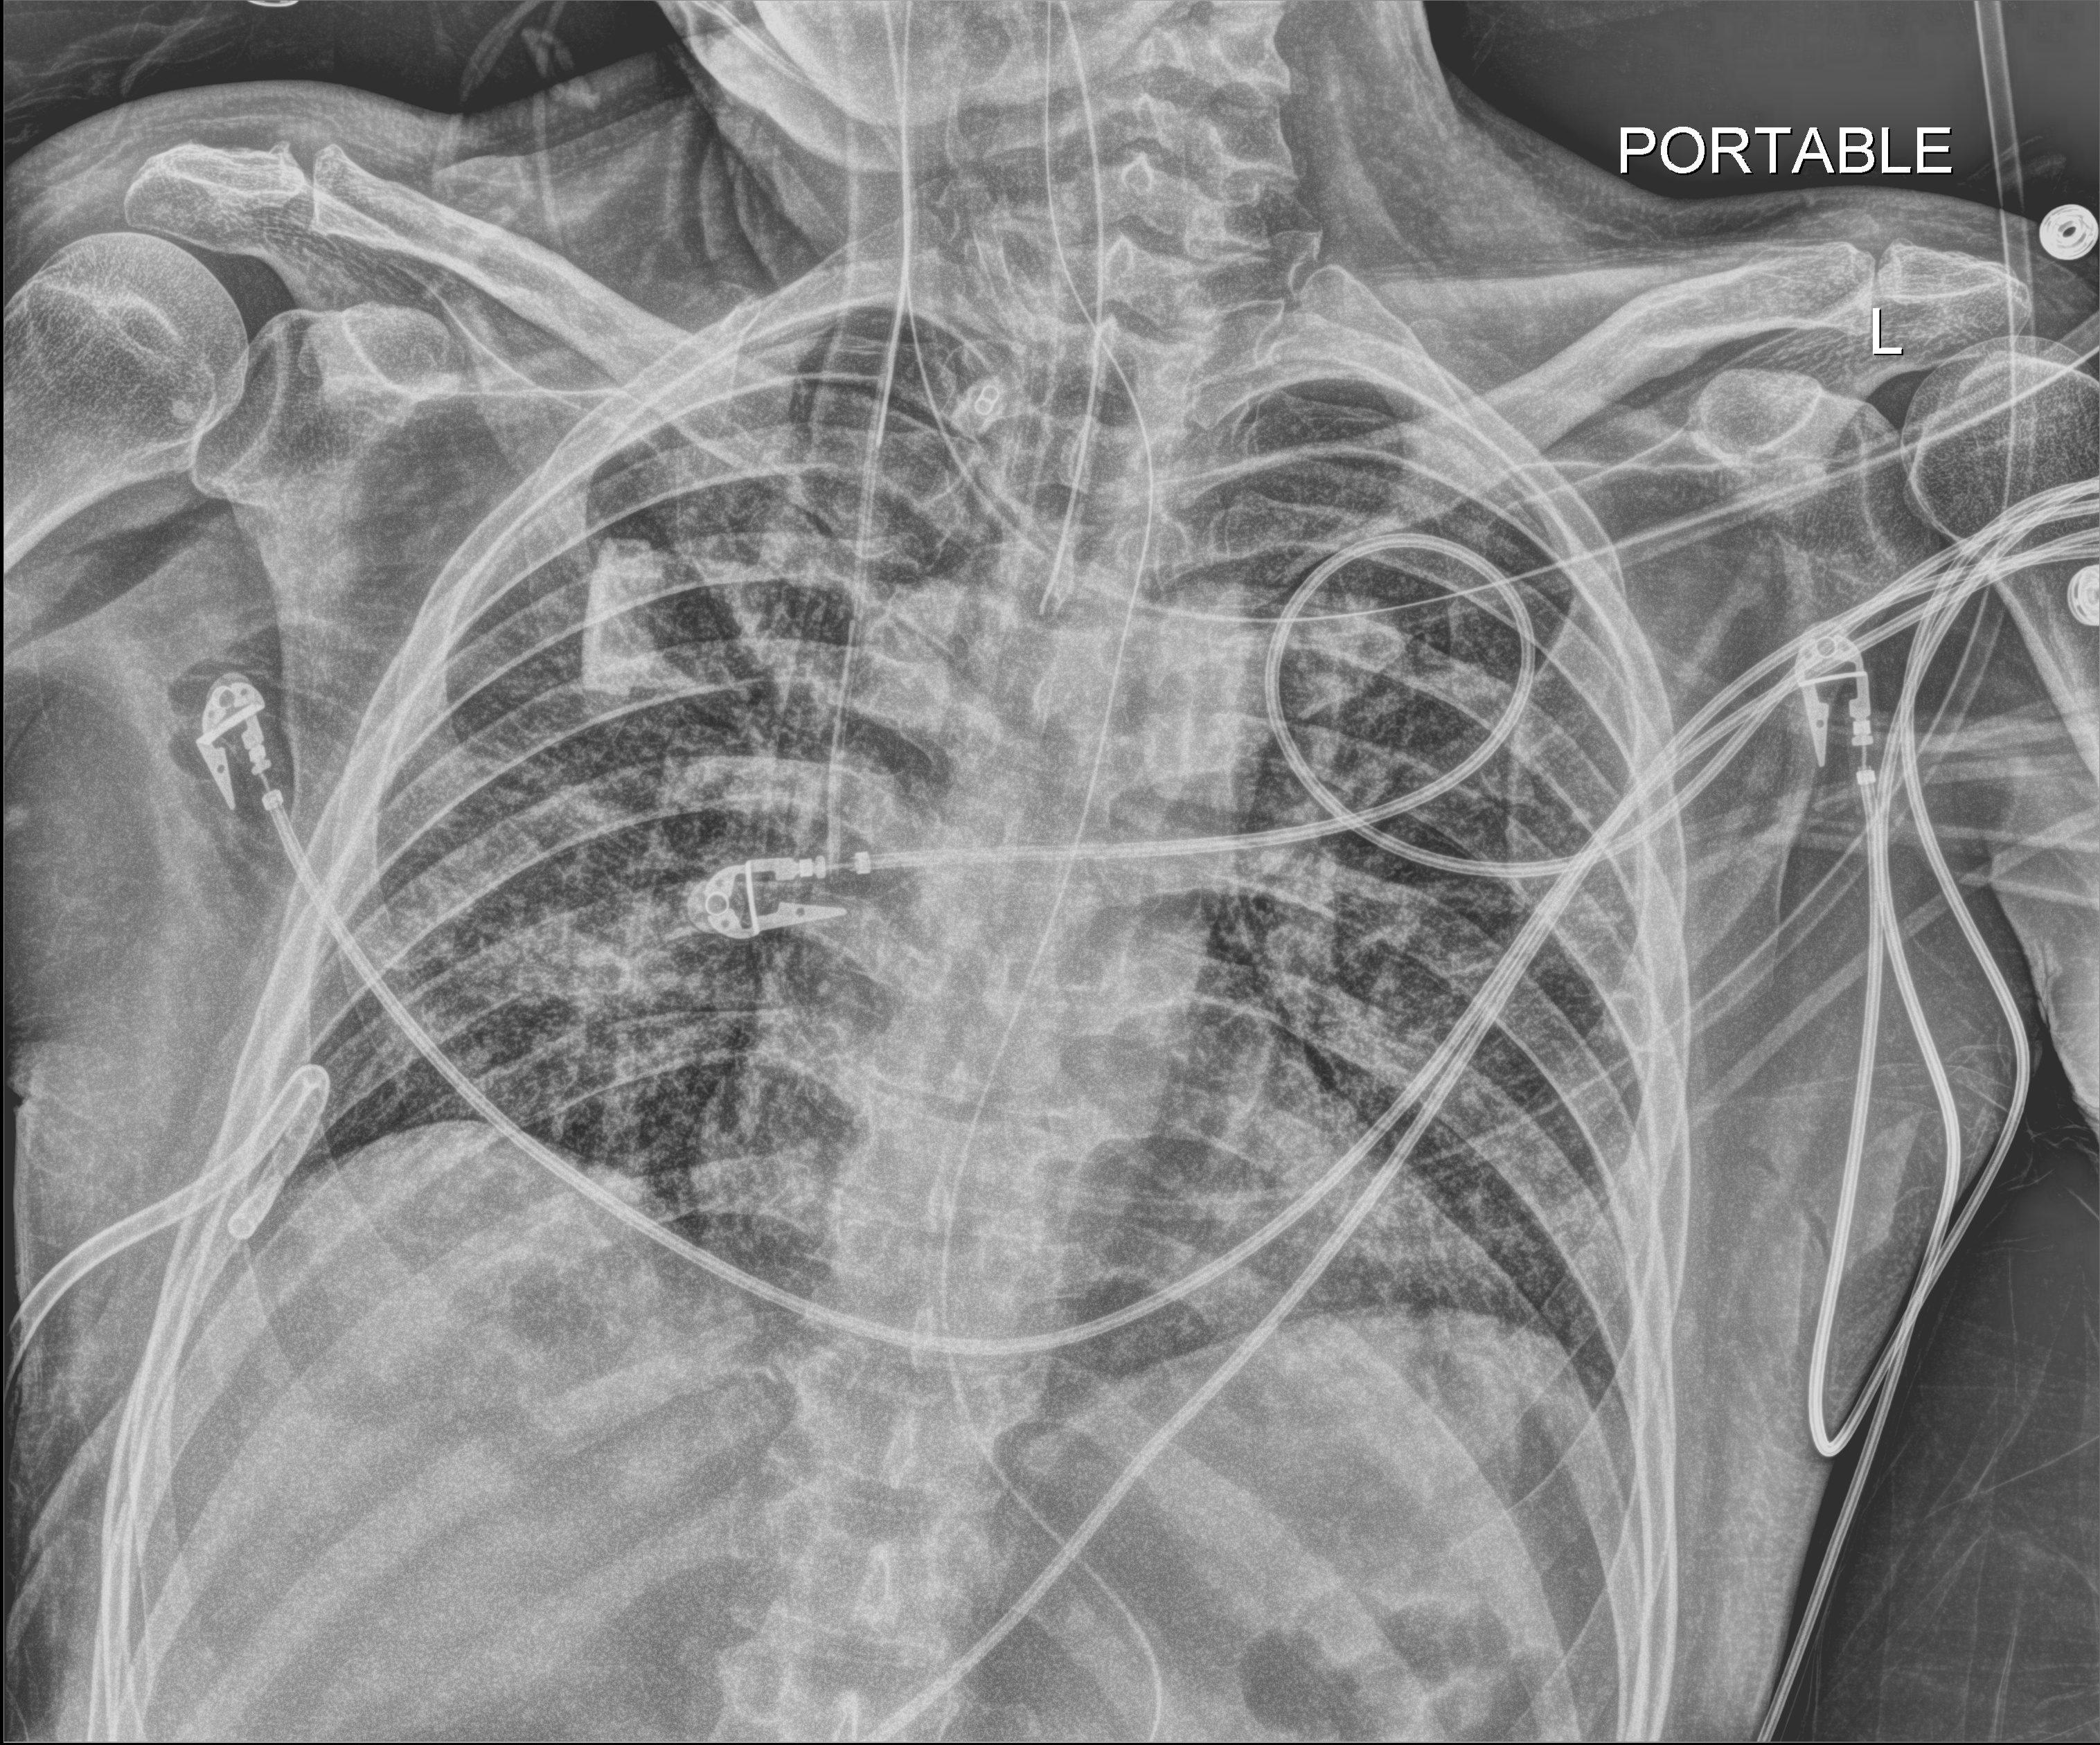
Chest X-ray (portable); anteroposterior (AP) projection. Patient hospitalised with COVID-19; male, aged 18–59 years.
From the hospital-stay record, not from the radiograph (when in the stay this image was taken is not recorded): hypertension (admission record): no.